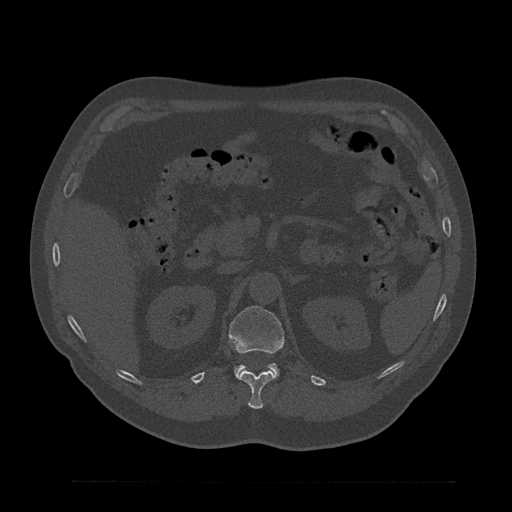
CT including the spine, one axial slice. Position 198 of 797 along the scan axis. Reconstruction kernel Br40s/3. 120 kVp. Bone window (W 1800 / L 400 HU). 512 × 512 image matrix, field of view 430 × 430 mm. Patient: male, 61 years. Case-level facts recorded for this patient, not image findings: primary cancer: prostate.
Outlined on this slice (semi-automatically segmented with operator editing):
- L1 vertebra: bounding box [x1, y1, x2, y2] px = [229, 306, 284, 377]
- T12 vertebra: [237, 370, 276, 409]